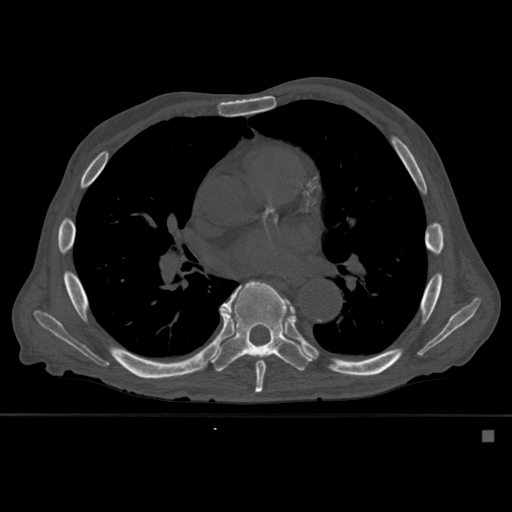
CT including the spine, one axial slice; position 356 of 527 along the scan axis; bone window (W 1800 / L 400 HU); 512 × 512 image matrix, field of view 373 × 373 mm. Patient: male, 78 years. Case-level facts recorded for this patient, not image findings: primary cancer: prostate.
Structures marked on this image (semi-automatically segmented with operator editing):
- T7 vertebra: bounding box (x1, y1, x2, y2) in pixels: (224, 281, 295, 393)
- T8 vertebra: (211, 281, 311, 372)